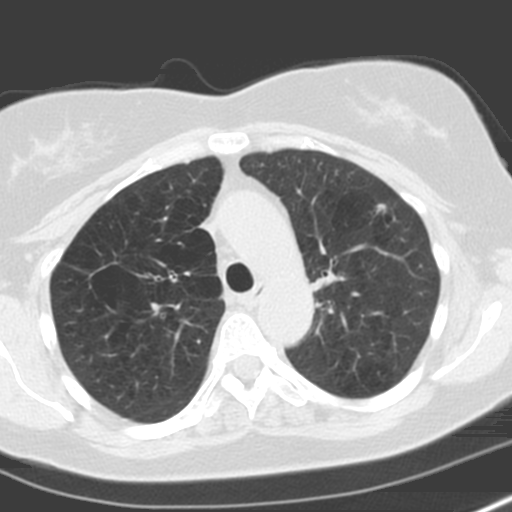
Low-dose screening chest CT, axial slice. First (baseline) screen. Lung window (W 1500 / L -600 HU). 3.2 mm slice thickness. 120 kVp. Slice 53 of 173 in the series. Female, age 57 years at enrolment. Former smoker at enrolment.
Expert-annotated lung lesion, bounding box <359,198,399,229> (left, top, right, bottom; pixels). No non-calcified nodule or mass ≥4 mm was recorded by the screening reader at this exam. Lung cancer was diagnosed 503 days after this screen: adenocarcinoma, NOS, left upper lobe, moderately differentiated (G2), stage IA (AJCC 6th edition), 18 mm at pathology.